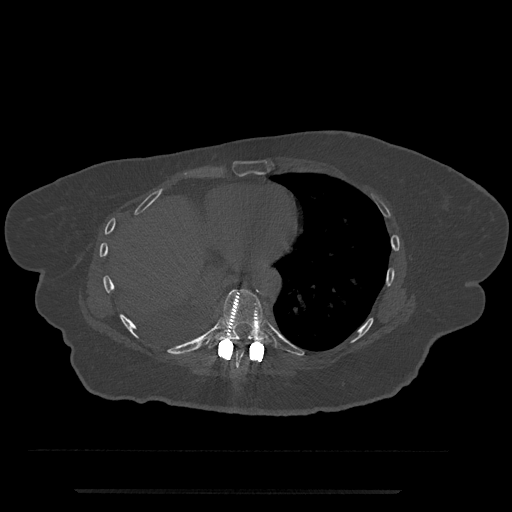
CT including the spine, one axial slice; position 355 of 797 along the scan axis; reconstruction kernel Br40s/3; 120 kVp; bone window (W 1800 / L 400 HU); 512 × 512 image matrix, field of view 440 × 440 mm. Female patient, age 51 years. Case-level facts recorded for this patient, not image findings: primary cancer: neuro; vertebrae with lytic lesions (as recorded): T8.
Annotated regions visible in this slice (semi-automatic segmentation, software-assisted and operator-edited):
- T8 vertebra: bounding box <231,347,263,373> (left, top, right, bottom; pixels)
- T9 vertebra: <207,289,275,348>